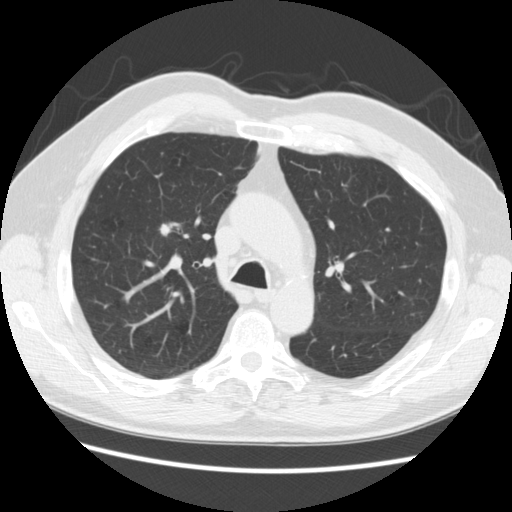
Low-dose screening chest CT, one axial slice. Slice 177 of 259 in the series (ordered by position). 120 kVp. Lung window (W 1500 / L -600 HU). 2.5 mm slice thickness. 512 × 512 image matrix, field of view 360 × 360 mm.
Outlined on this slice (expert manual segmentation):
- lesion 1 (tumor, upper lobe of right lung): bounding box (x1, y1, x2, y2) in pixels: (159, 224, 172, 236)